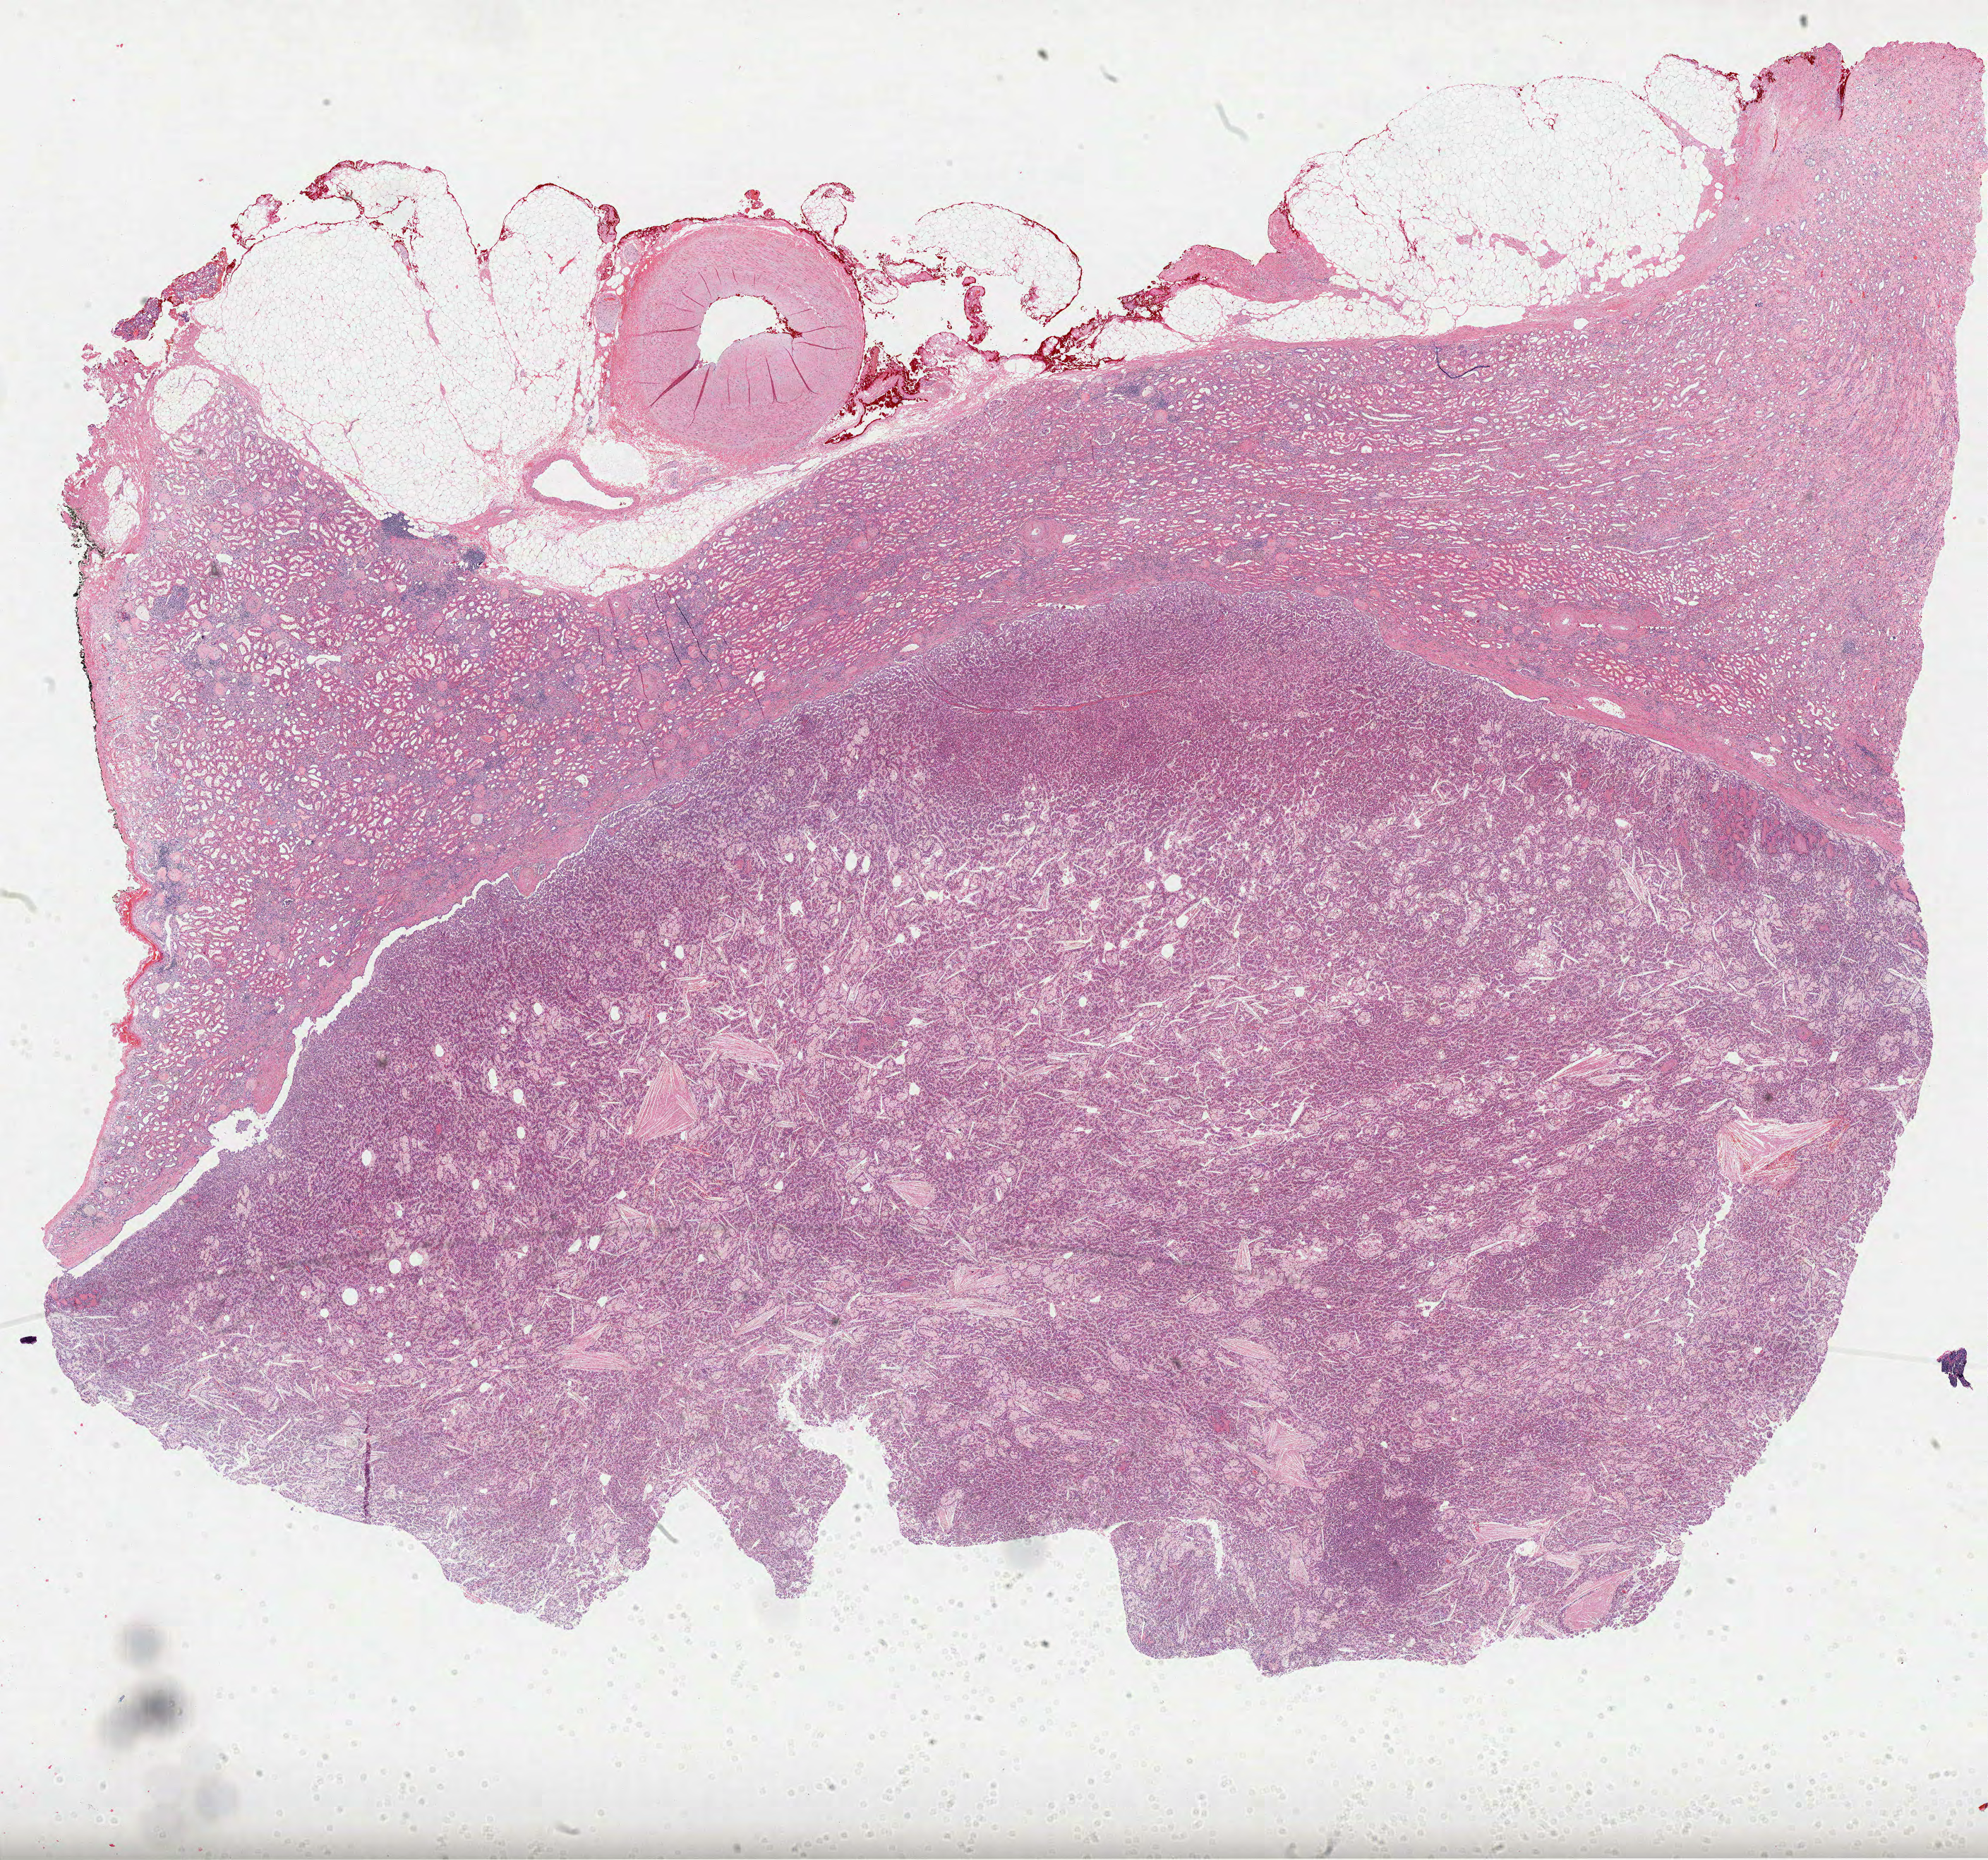
Whole-slide histology image, H&E-stained, a low-resolution overview of the entire scanned area, about 22.7 x 21.3 mm, formalin-fixed paraffin-embedded (FFPE) diagnostic section, primary tumour sample from the kidney. Patient: male, age at initial diagnosis 57 years.
Laterality: left. Diagnosis: Papillary adenocarcinoma, NOS. AJCC pathologic stage: I (7th edition).